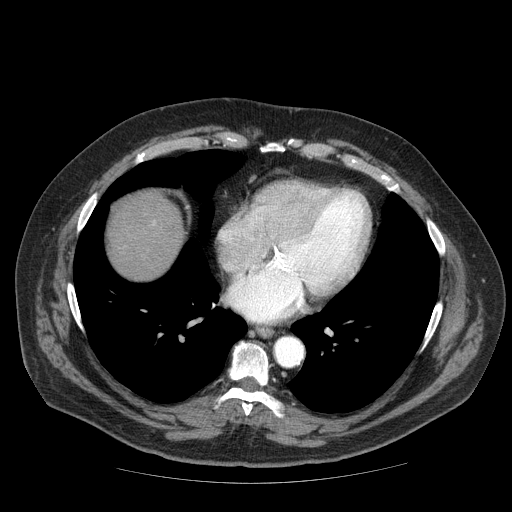
Contrast-enhanced abdominal CT (liver protocol), one axial slice; slice 72 of 85 in the series (ordered by position); reconstruction kernel STANDARD; soft-tissue window (W 400 / L 40 HU); 512 × 512 image matrix. From the clinical record (not read from this slice): diagnosis: hepatocellular carcinoma (patient treated with transarterial chemoembolisation; whether this scan precedes or follows treatment is not stated here); TNM stage (as recorded): Stage-IIIA; Child-Pugh class: A; tumour nodularity: multinodular; tumour size: 7 cm.
Outlined on this slice (semi-automatic segmentation, software-assisted and operator-edited):
- liver parenchyma outside the tumour (the mass and vessels are separate outlines, so this box may not span the whole liver): bounding box <108,190,184,280> (left, top, right, bottom; pixels)